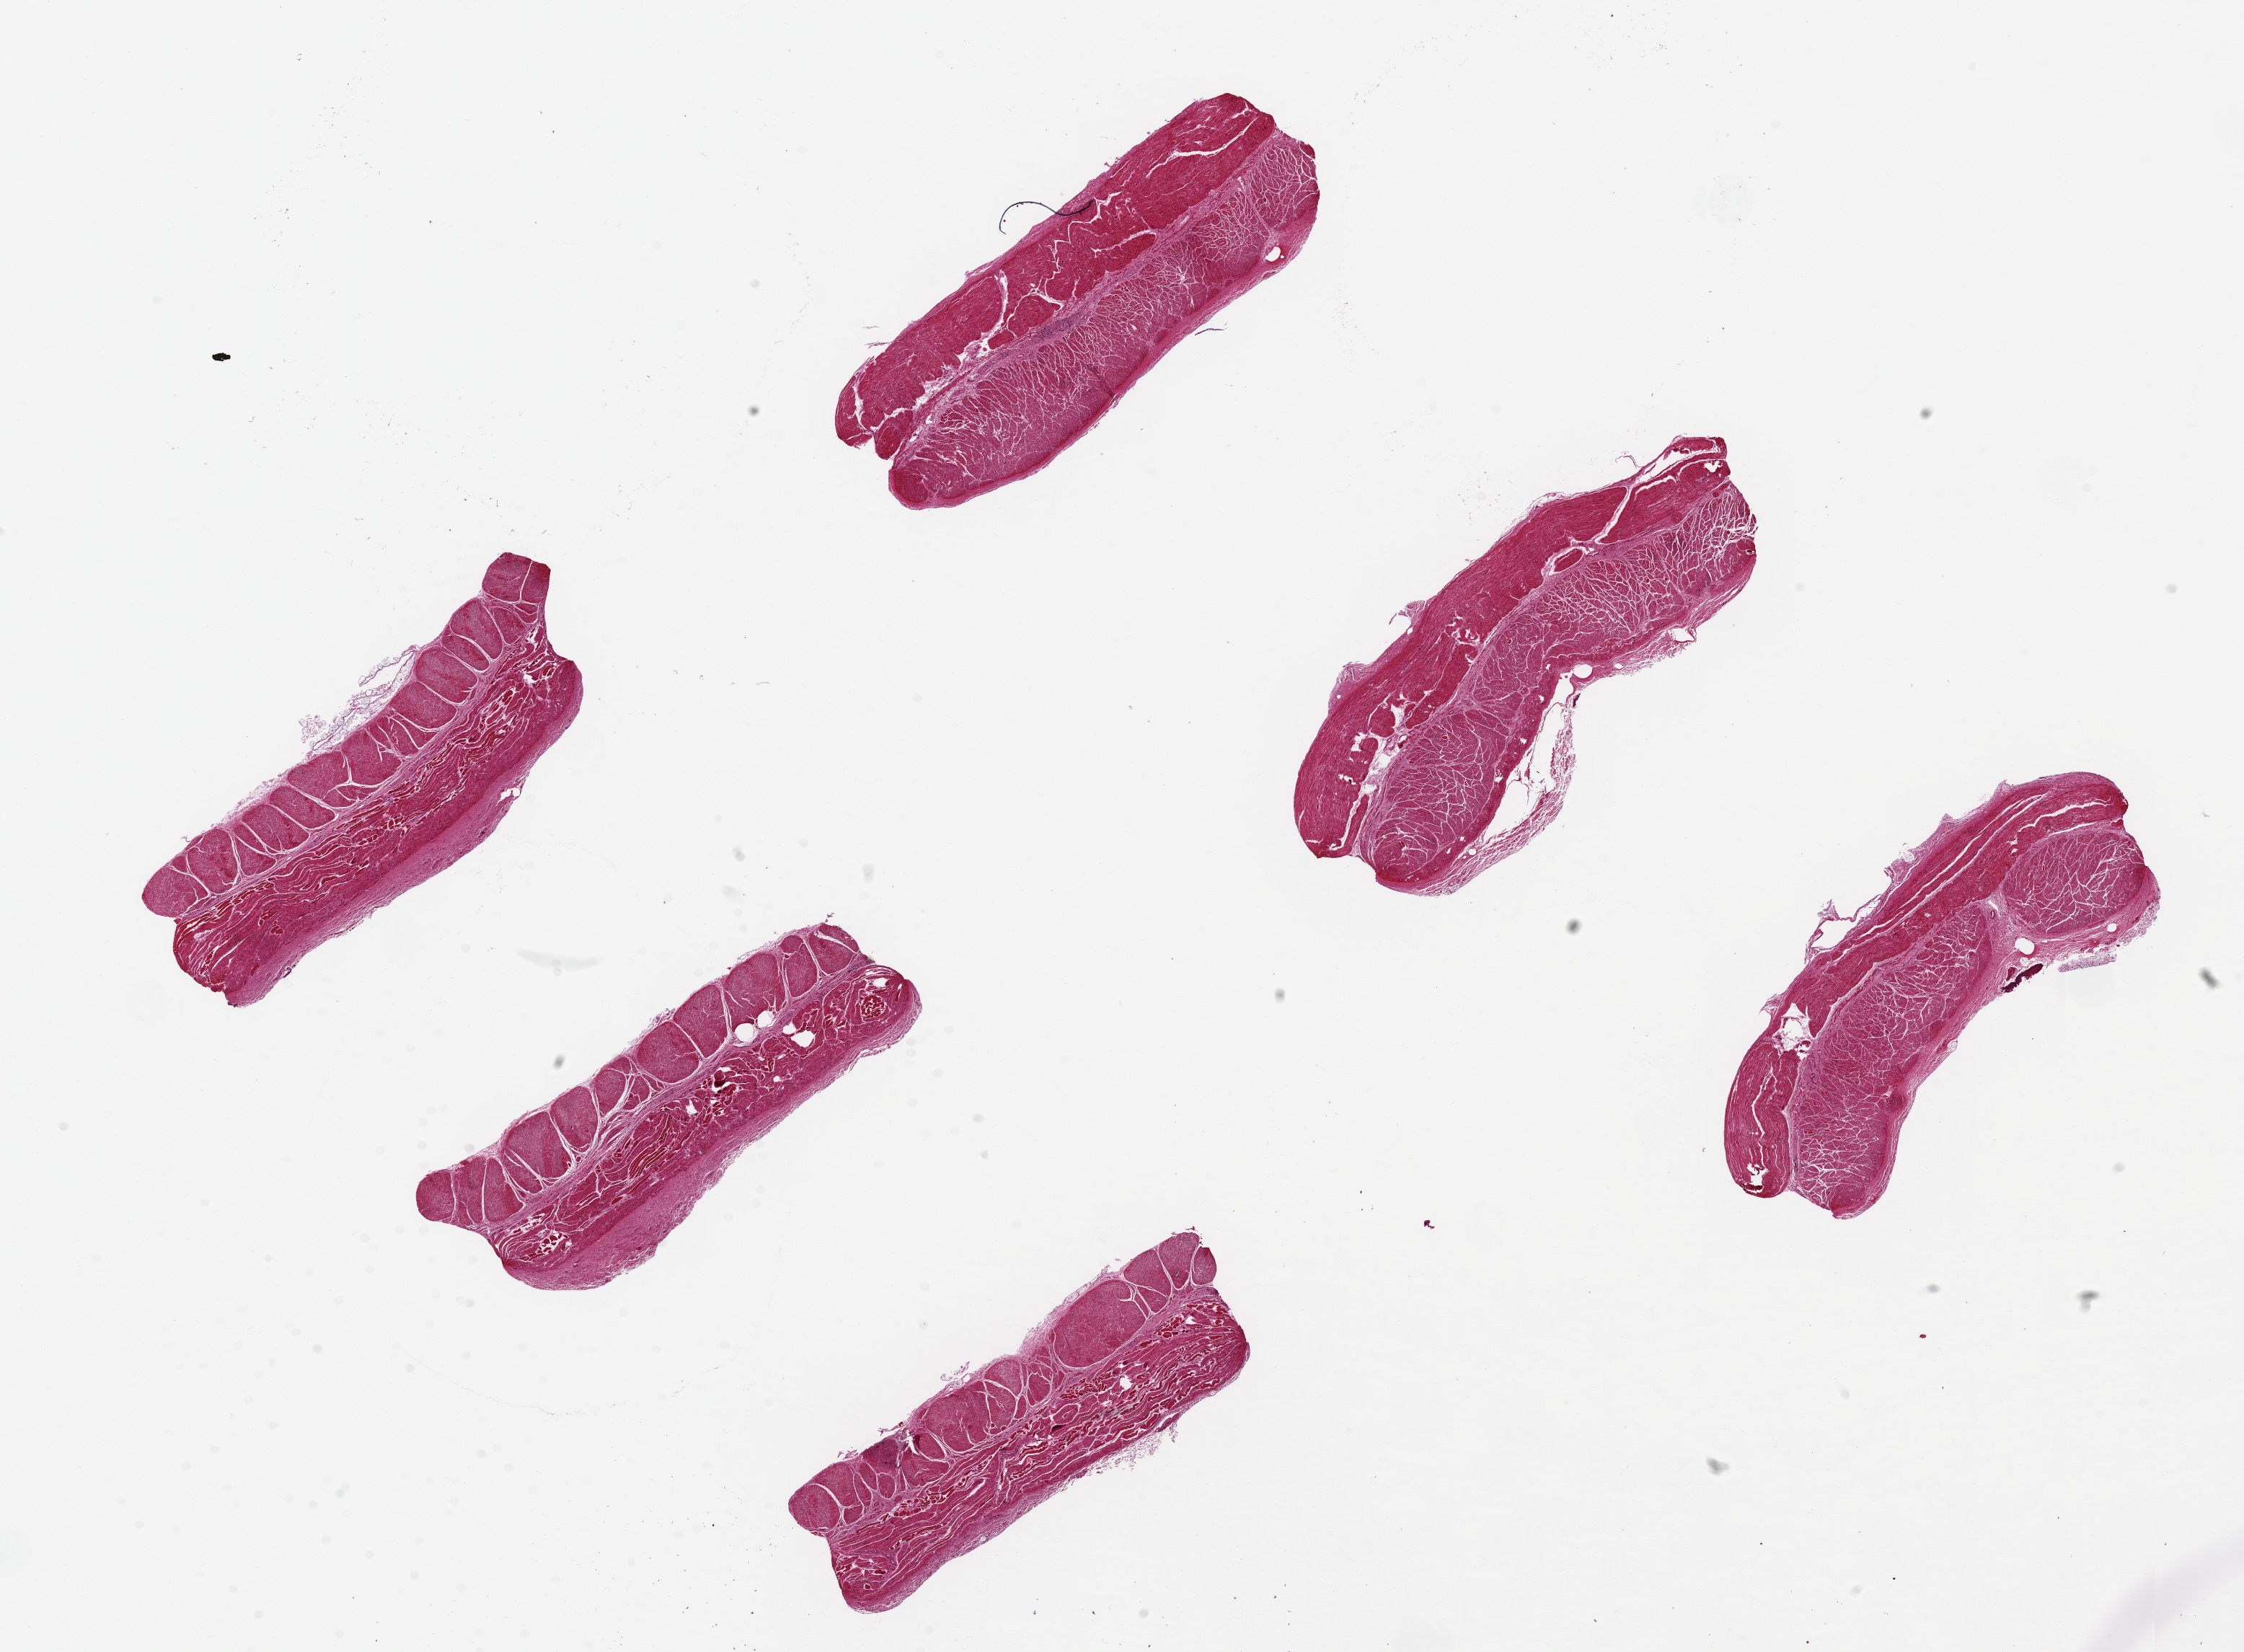
Digitized hematoxylin and eosin (H&E)-stained section, low-resolution overview of the scanned area, about 24.6 x 18.1 mm (acquisition: 20x scan). PAXgene-fixed, paraffin-embedded tissue. Target tissue: esophageal muscle. Tissue donor sample. Male donor.
Pathologist's review note for this sample: 6 pieces, ~5.5x1.5mm.